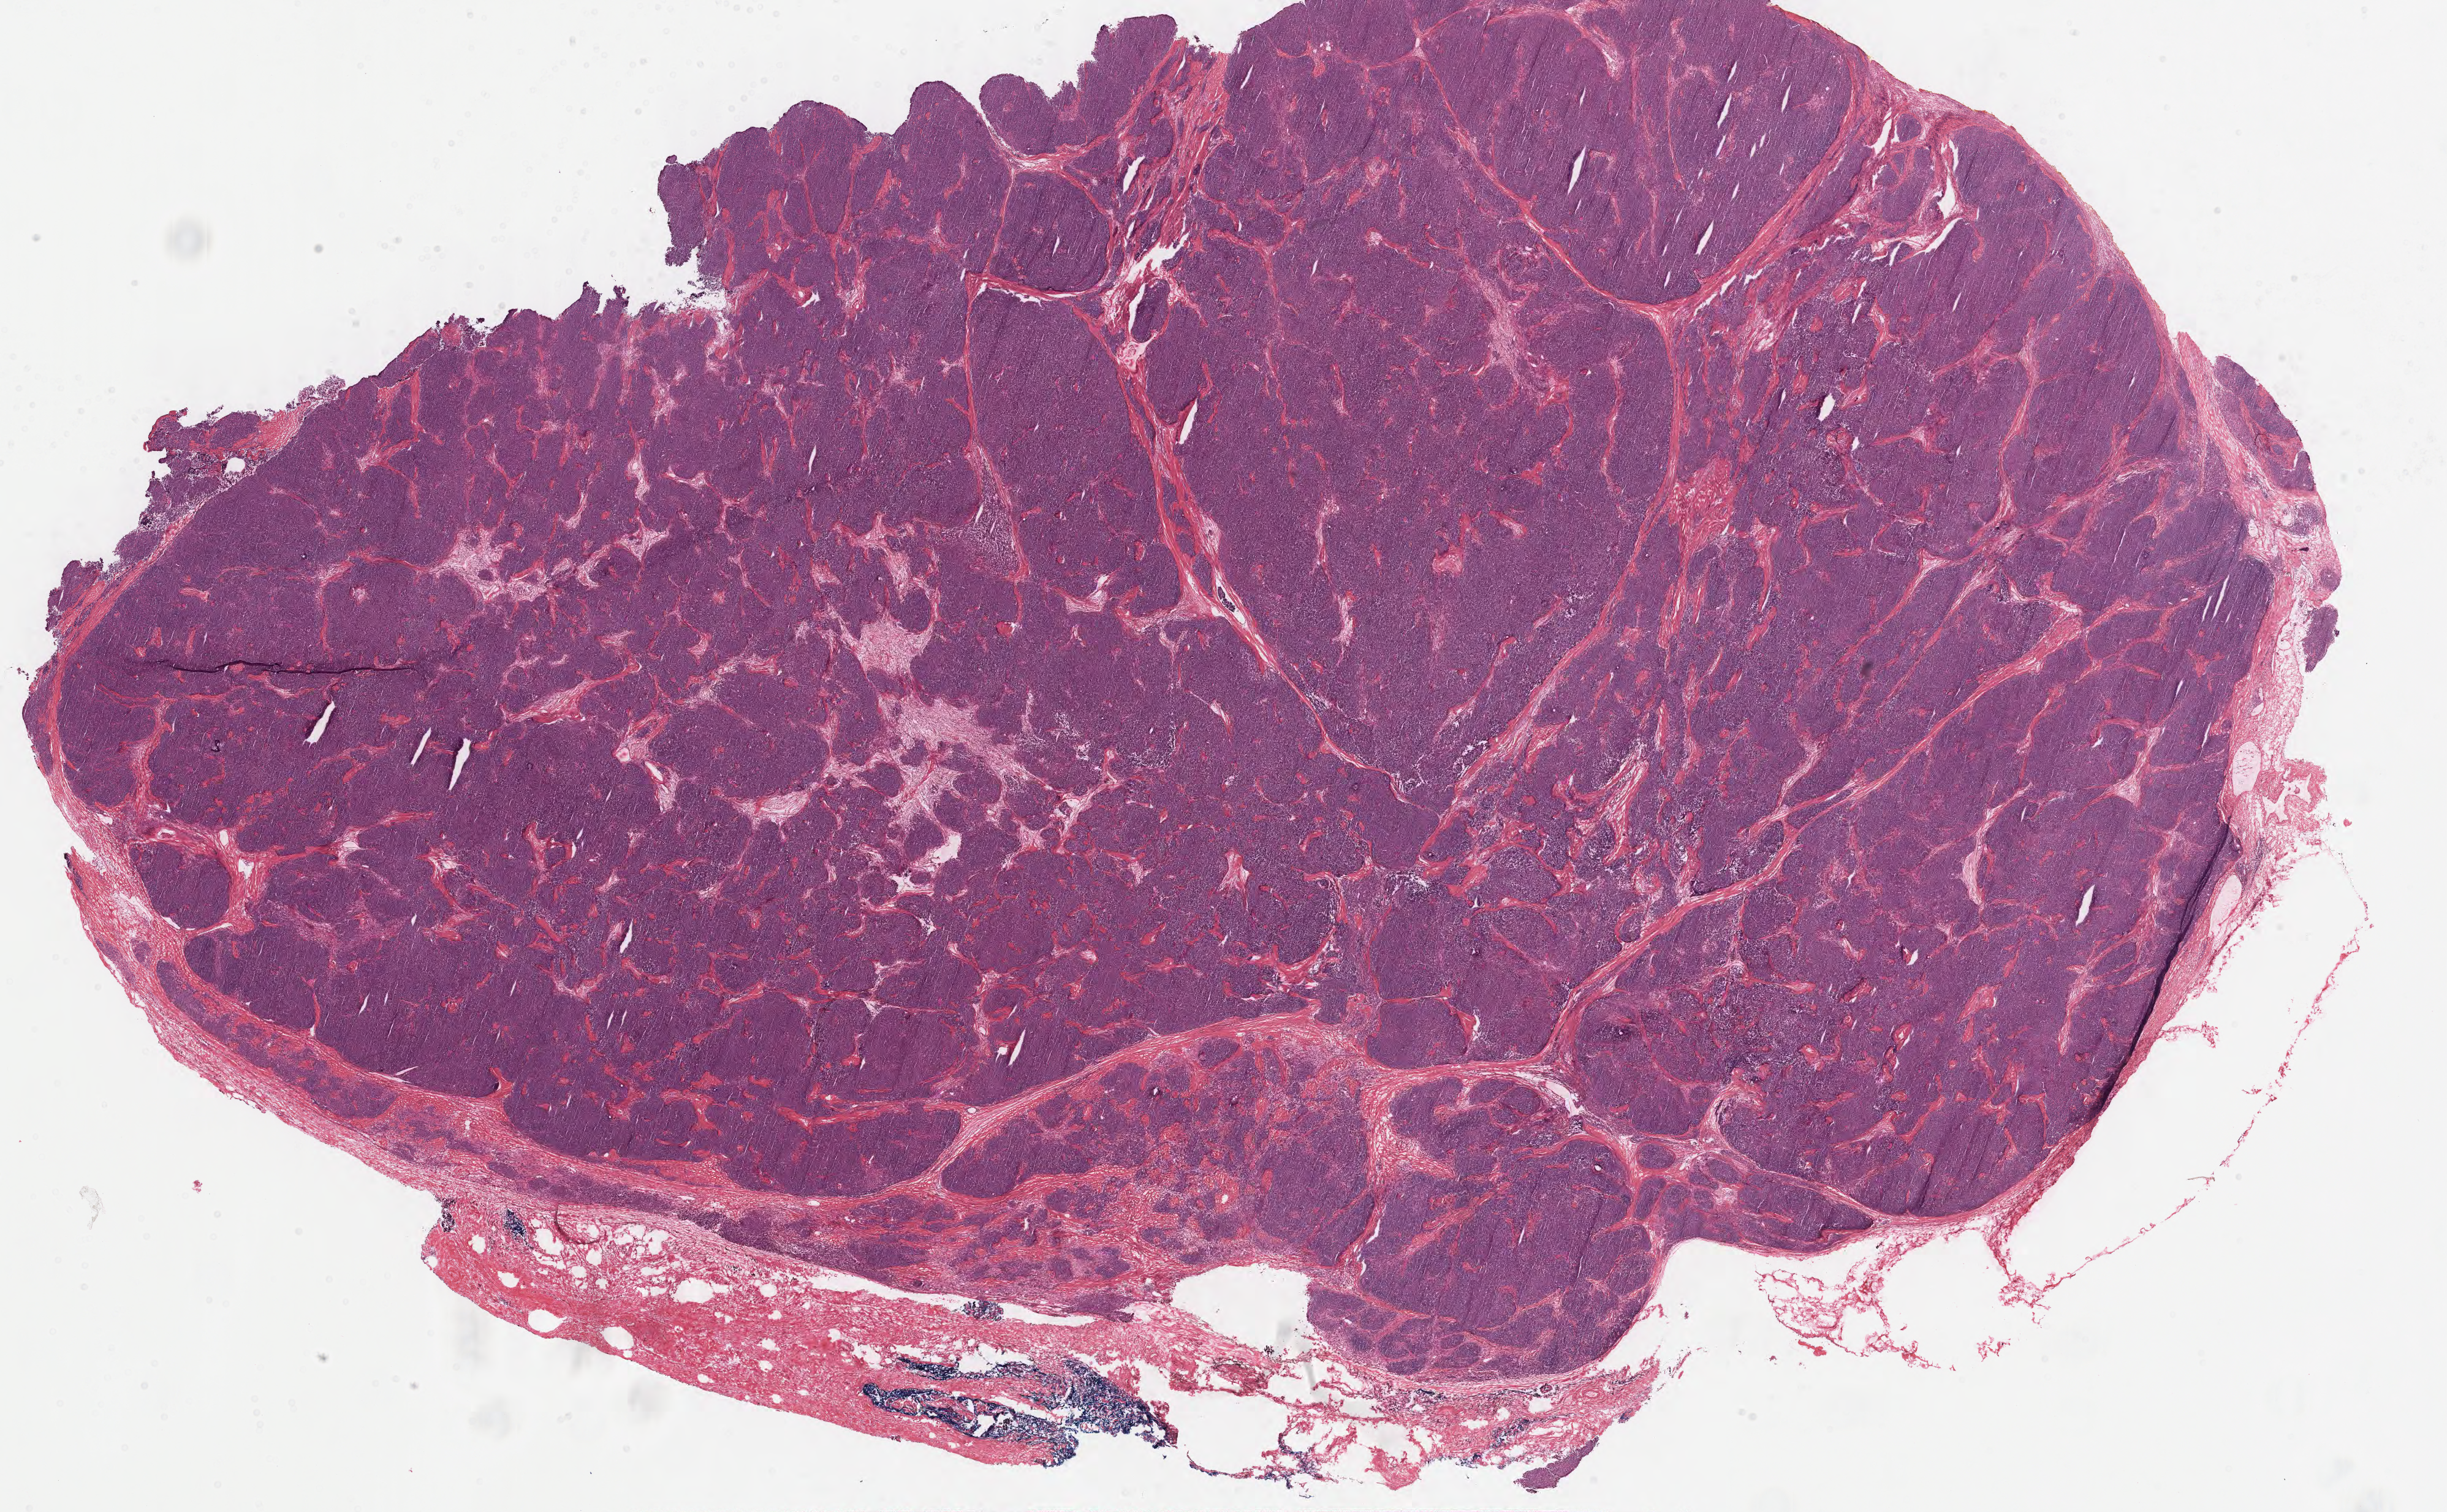
Hematoxylin and eosin (H&E) stained whole-slide image — low-resolution overview of the scanned area, about 31.7 x 19.6 mm (acquisition: 40x scan); formalin-fixed paraffin-embedded (FFPE) diagnostic section; thymus, primary tumour sample. Female patient; age at initial diagnosis 50 years.
* histologic diagnosis: Thymoma, type AB, malignant